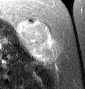
MRI of an extremity soft-tissue mass, one axial slice; slice 24 of 46 in the series (ordered by position); T2-weighted fat-saturated; MR volume resampled by the dataset authors to the PET/CT grid (not the native acquisition matrix); 3.27 mm slice thickness; 85 × 89 image matrix, field of view 83 × 87 mm. Female patient. From the clinical record (not read from this slice): histological type: leiomyosarcoma; grade: intermediate; site of the primary tumour: parascapusular.
Structures marked on this image (expert contour drawn on MRI and transferred to this co-registered scan by the dataset authors):
- gross tumour volume including surrounding oedema: box from (x=18, y=19) to (x=58, y=63) px
- gross tumour volume (mass): (x=20, y=21)–(x=51, y=56)